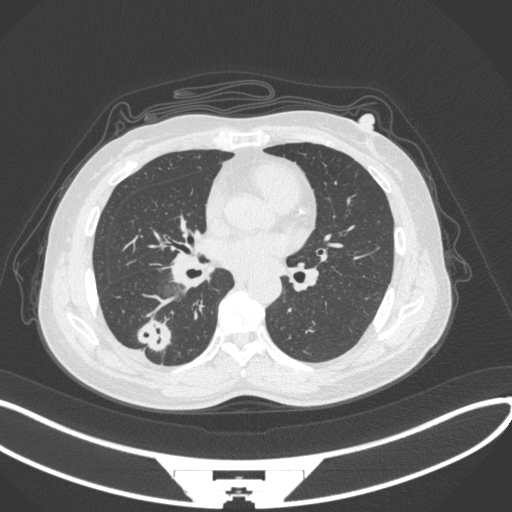
Chest CT, one axial slice. Slice 145 of 352 in the series (ordered by position). Reconstruction kernel B31f. Lung window (W 1500 / L -600 HU). 1 mm slice thickness. 512 × 512 image matrix, field of view 400 × 400 mm. Patient: female, 55 years. Case-level facts recorded for this patient, not image findings: clinical TNM (as recorded): T1c N1 M0.
Outlined on this slice (rectangle marked by the reading radiologist):
- lung tumour (recorded histology: adenocarcinoma): bounding box (x1, y1, x2, y2) in pixels: (132, 308, 175, 353)